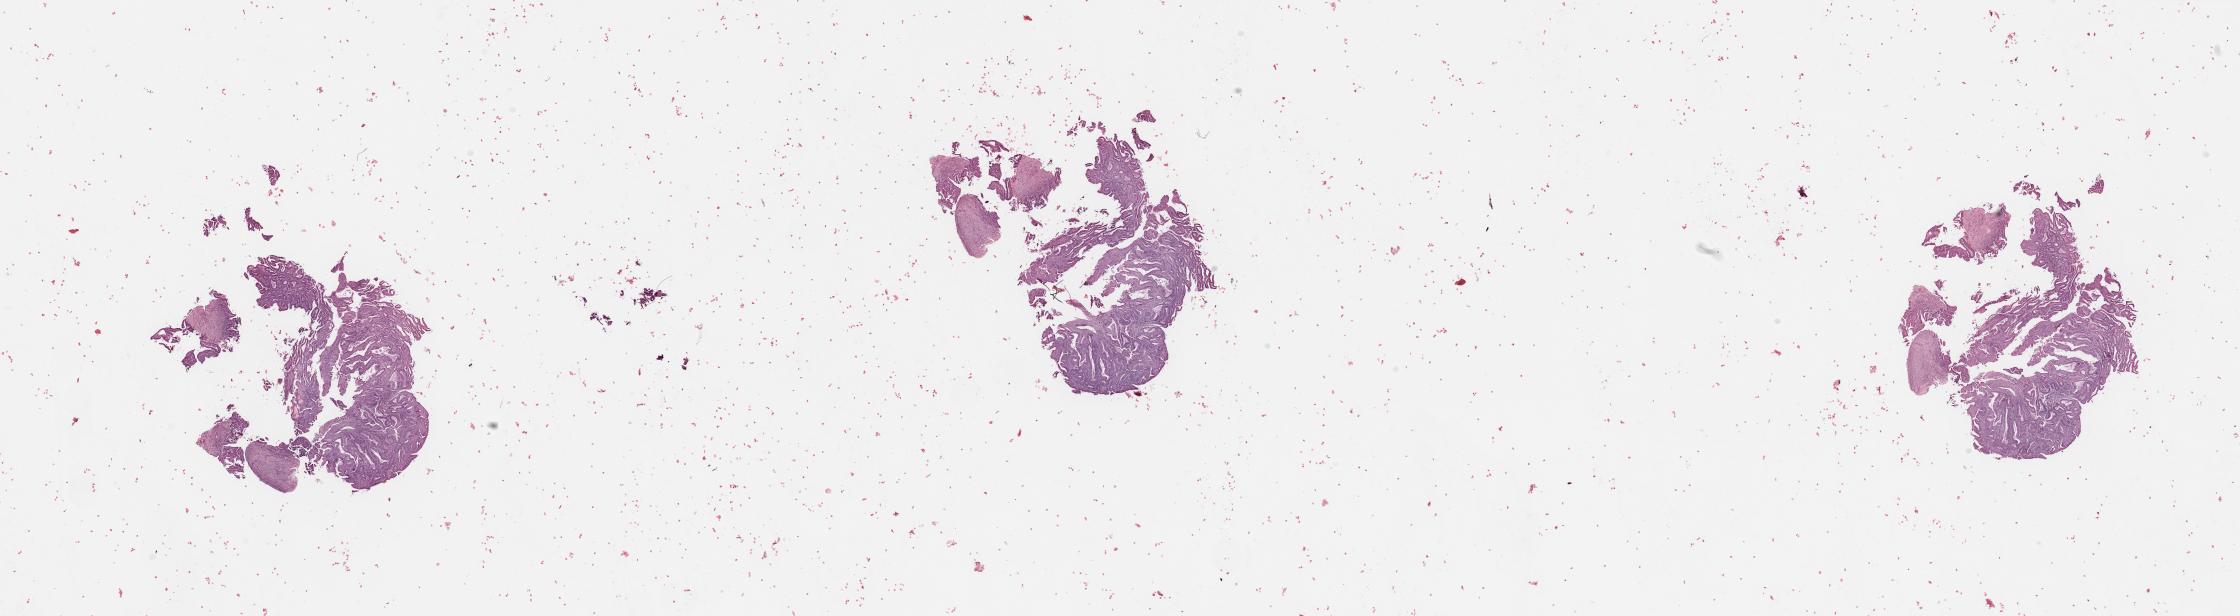
Whole-slide histology image, H&E — shown as a low-resolution overview of the whole scanned area (about 35.4 x 9.7 mm), tumour tissue sample, sampled site: uterus. Female, 72 y/o.
Diagnosis: Endometrioid adenocarcinoma, NOS.